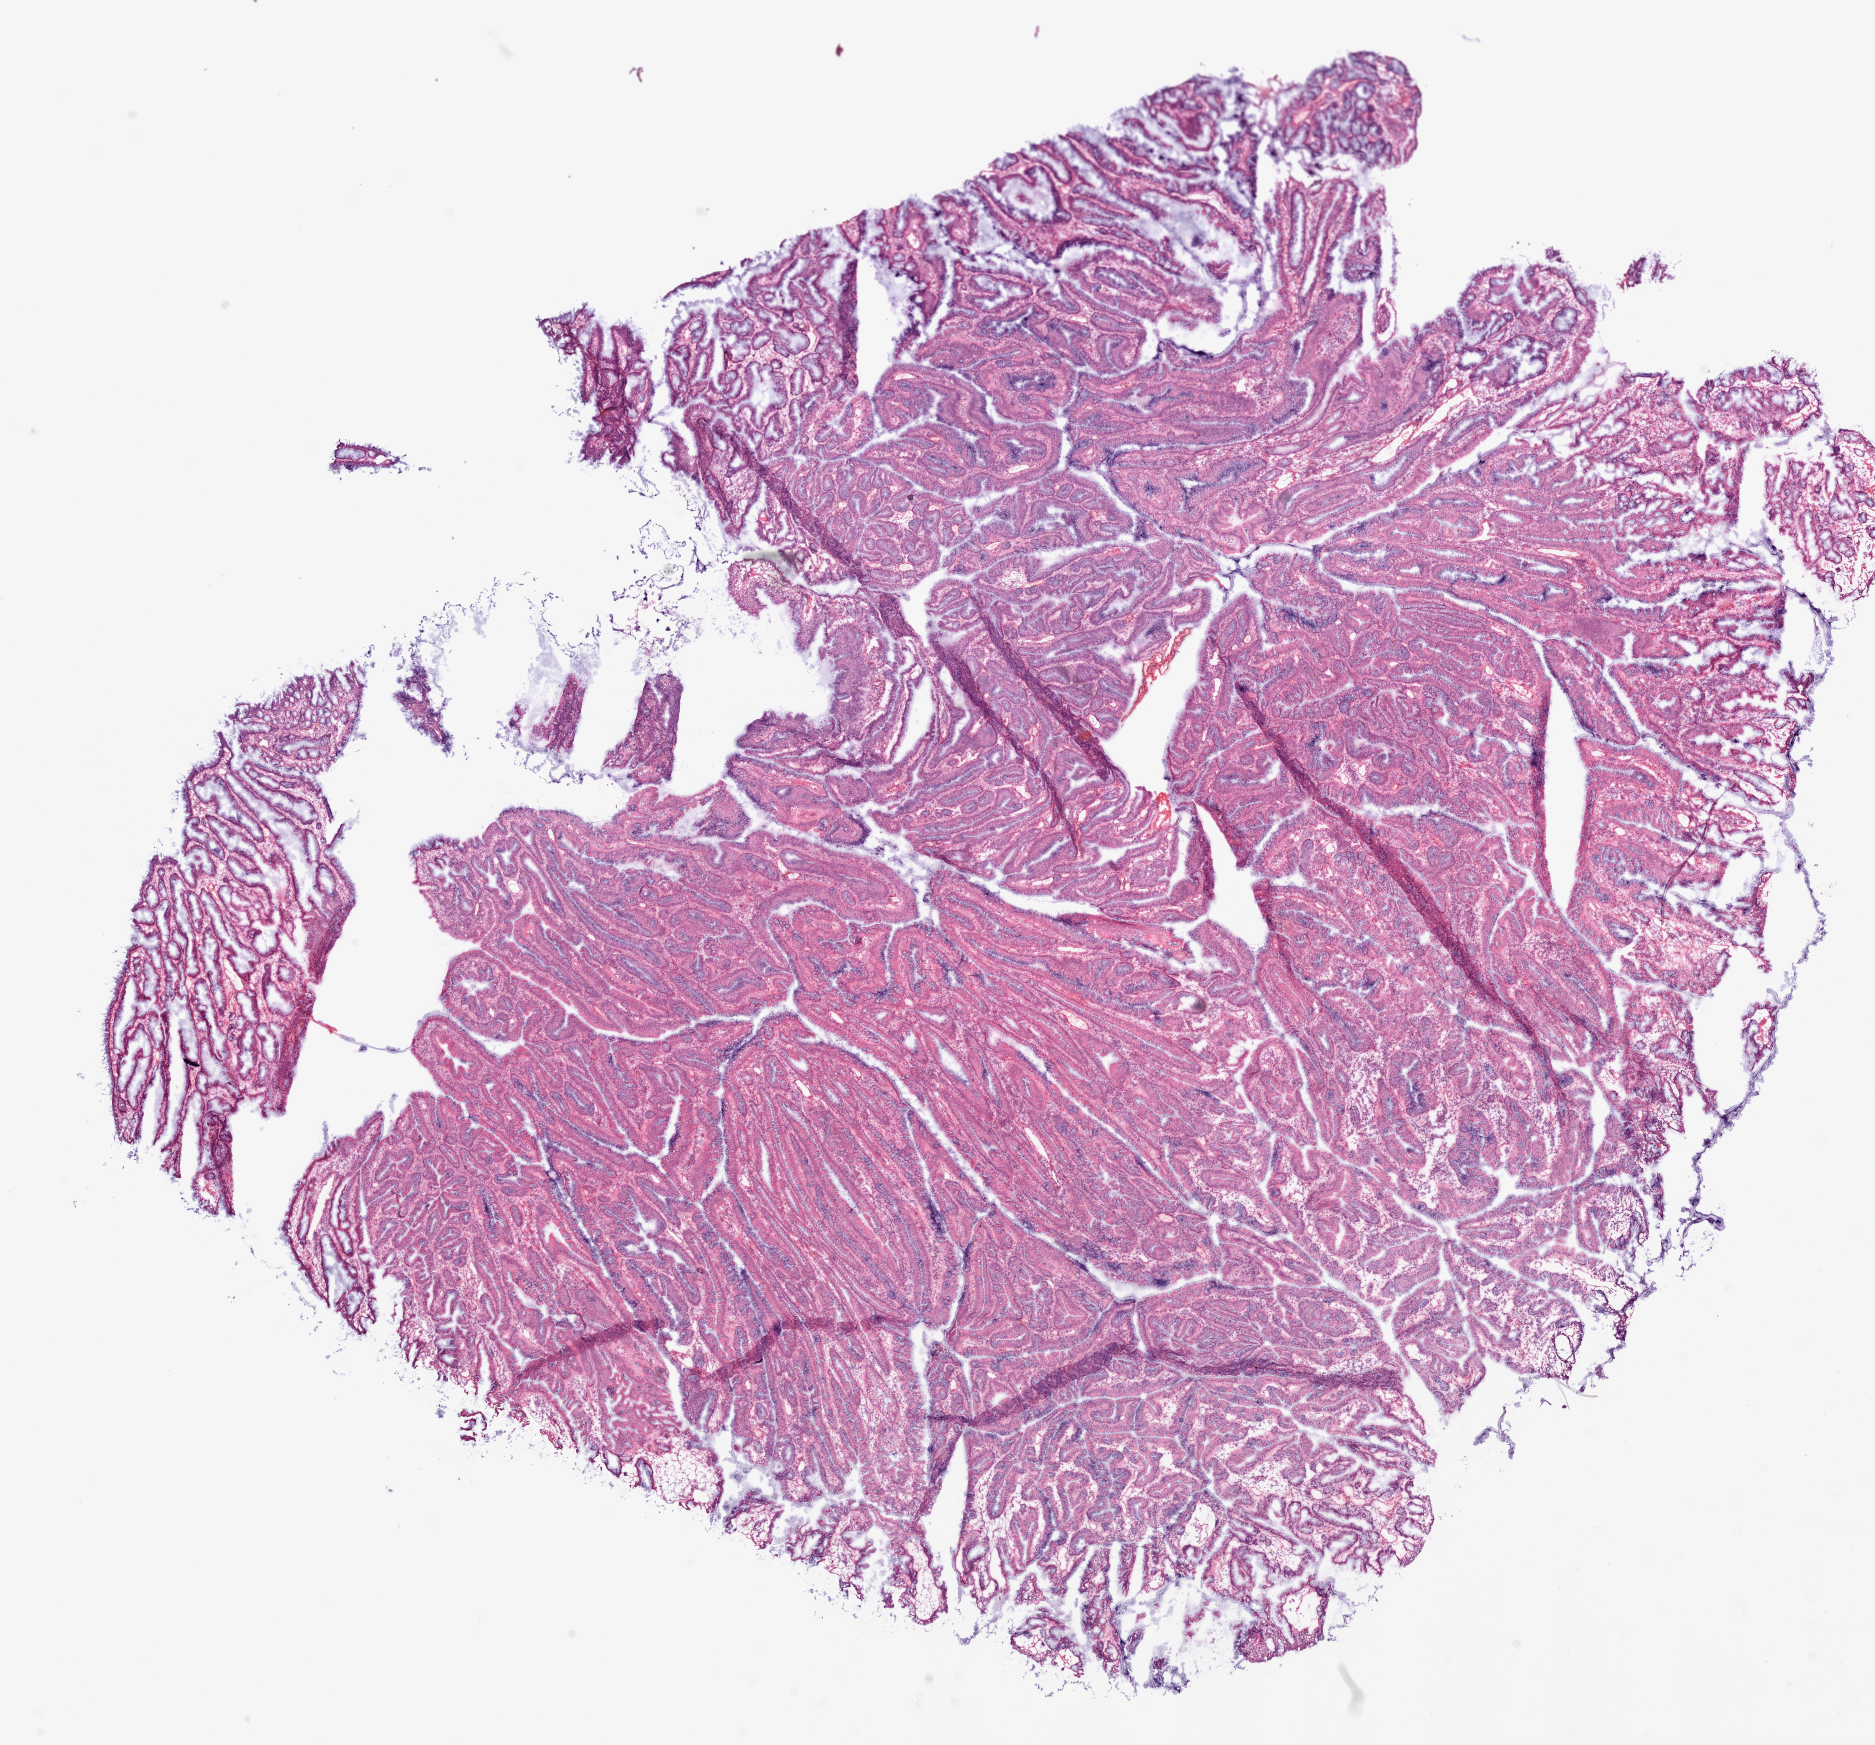
H&E-stained whole-slide image — whole scanned area (about 15.0 x 14.0 mm, from a 20x scan) shown as a low-resolution overview, frozen section from the top of the tissue portion, primary tumour sample from the colon. Female, age 52 years at initial diagnosis. Composition of this section per pathologist review: tumour cells 90%, tumour nuclei 80%, normal cells 0%, stromal cells 10%, necrosis 0%.
* histologic diagnosis: Mucinous adenocarcinoma (ascending colon)
* AJCC pathologic stage: IIA (6th edition)